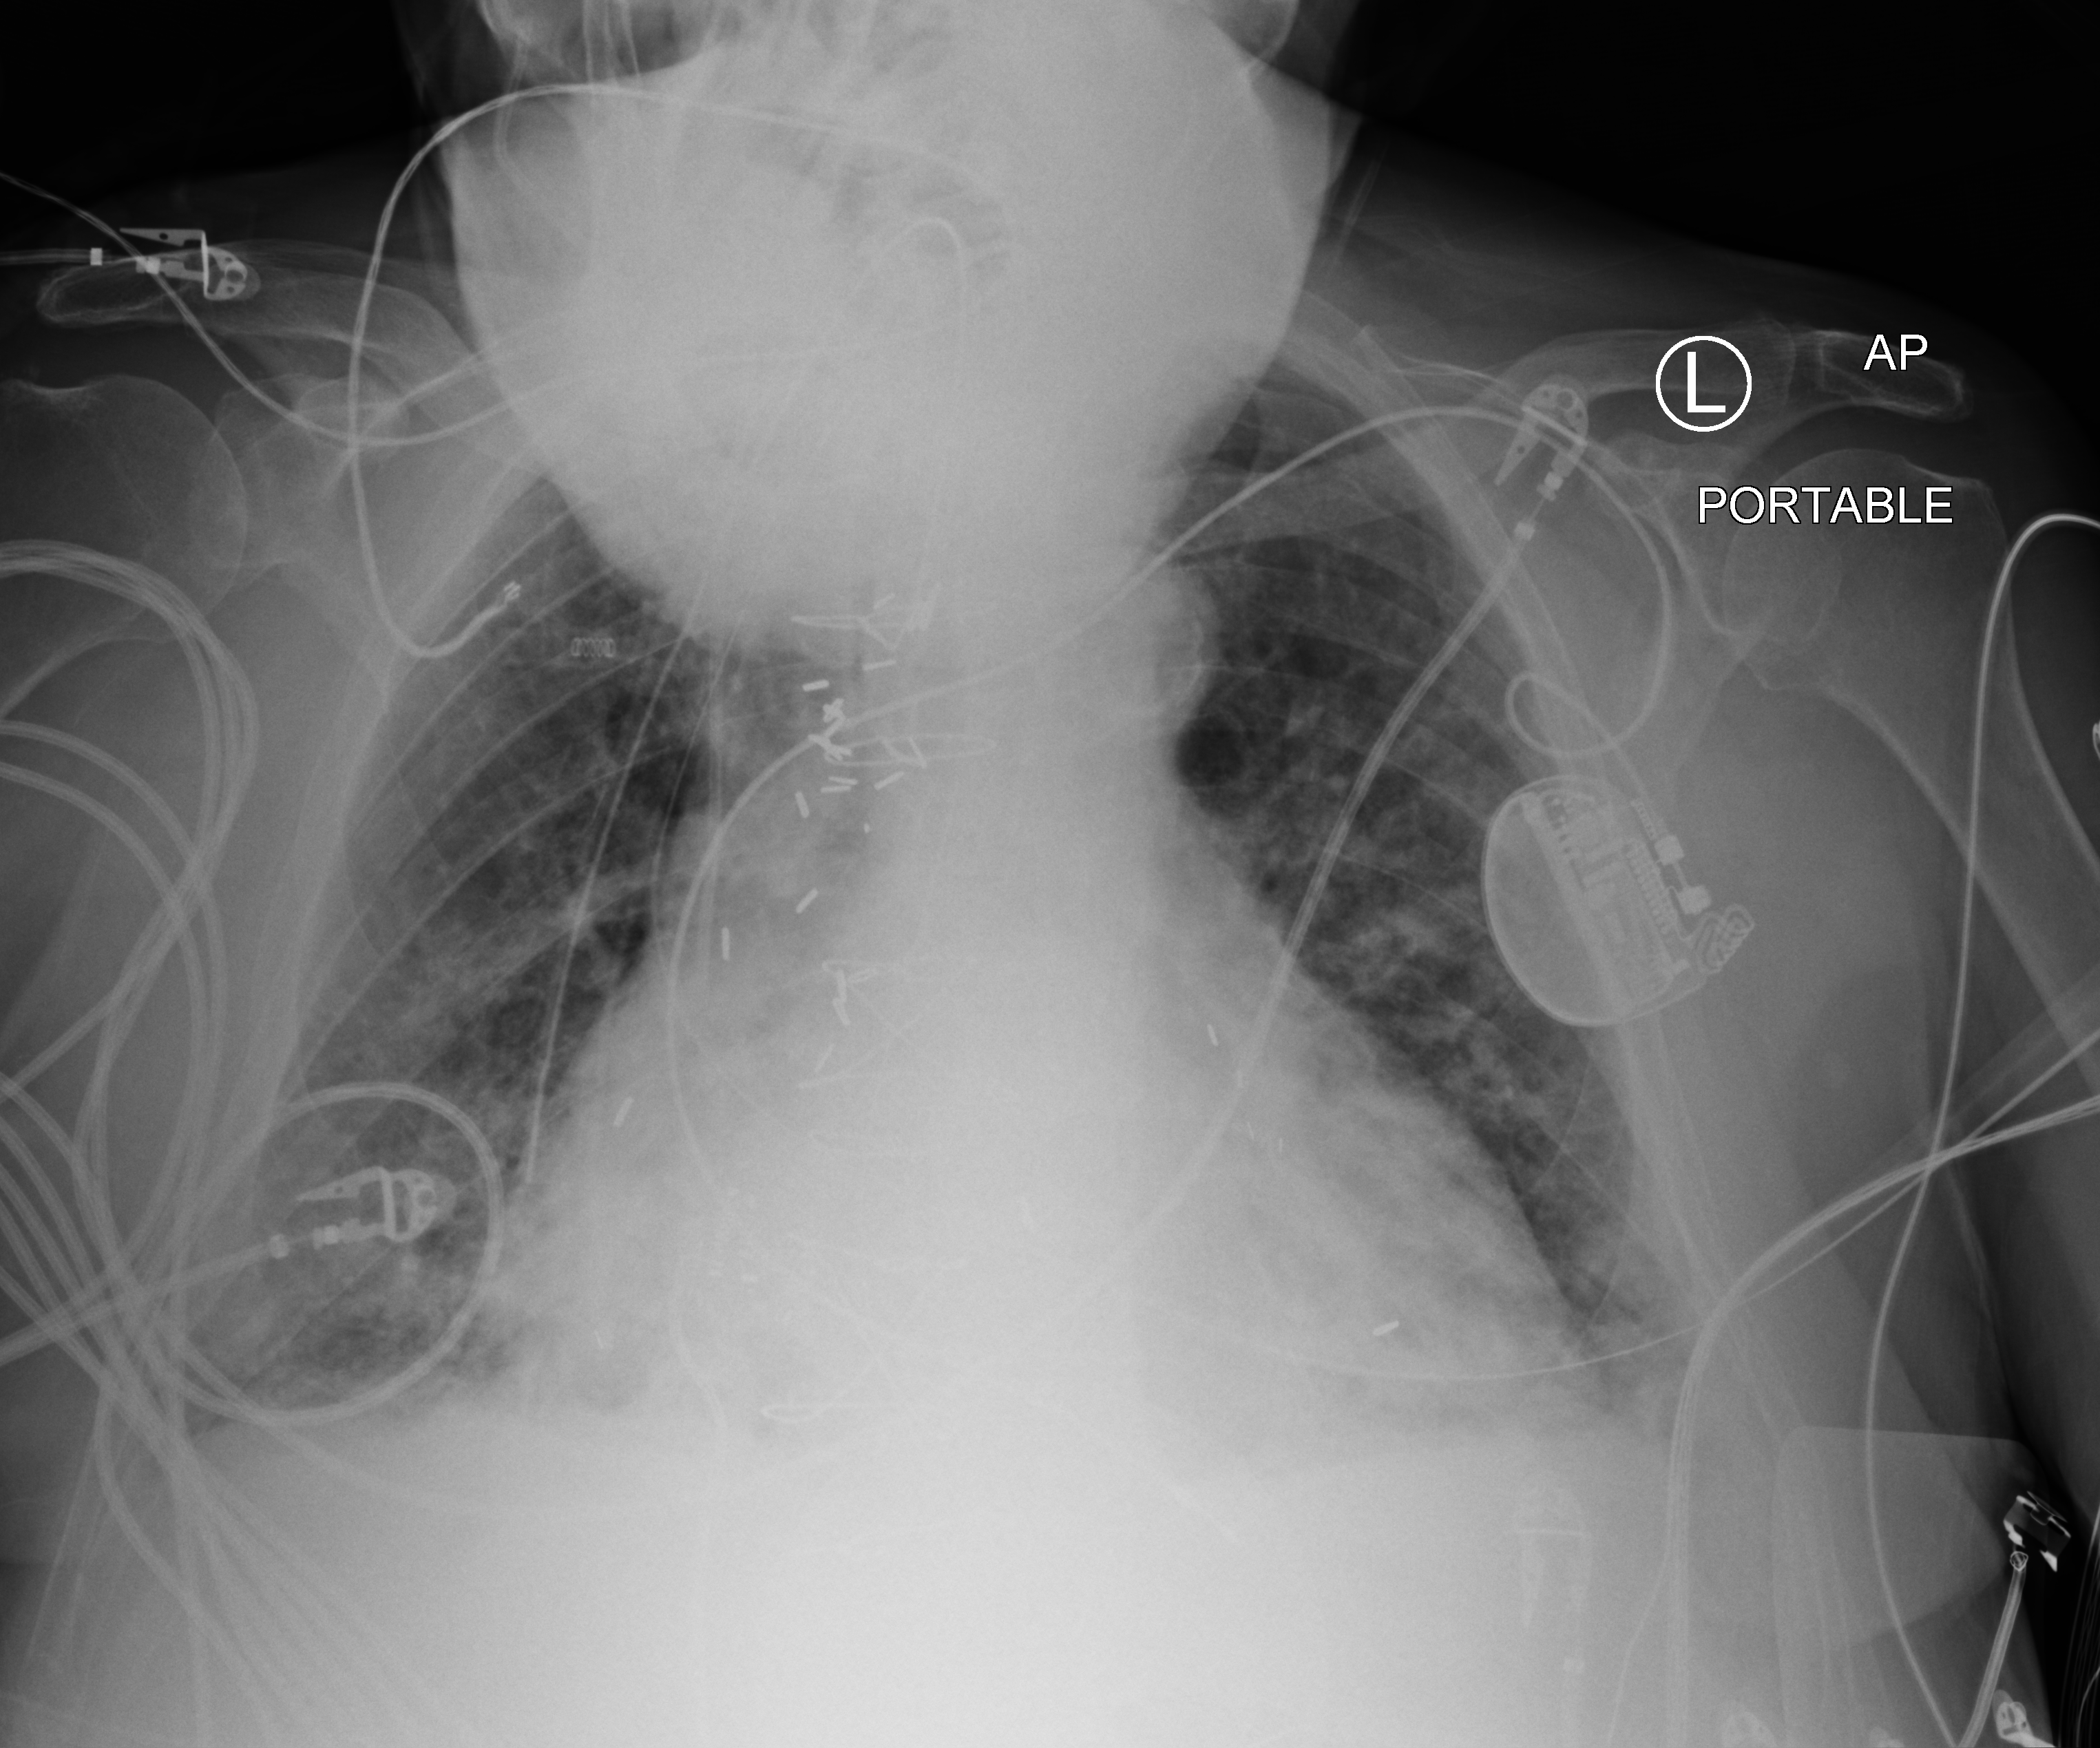
Chest X-ray (portable), anteroposterior (AP) projection. Male patient hospitalised with COVID-19, age 75–90 years.
Hospital-stay facts (about this admission, not read from this image; timing relative to this image not recorded):
- smoking status (admission record): former
- mechanically ventilated during this hospital stay: yes
- admitted to intensive care during this hospital stay: yes